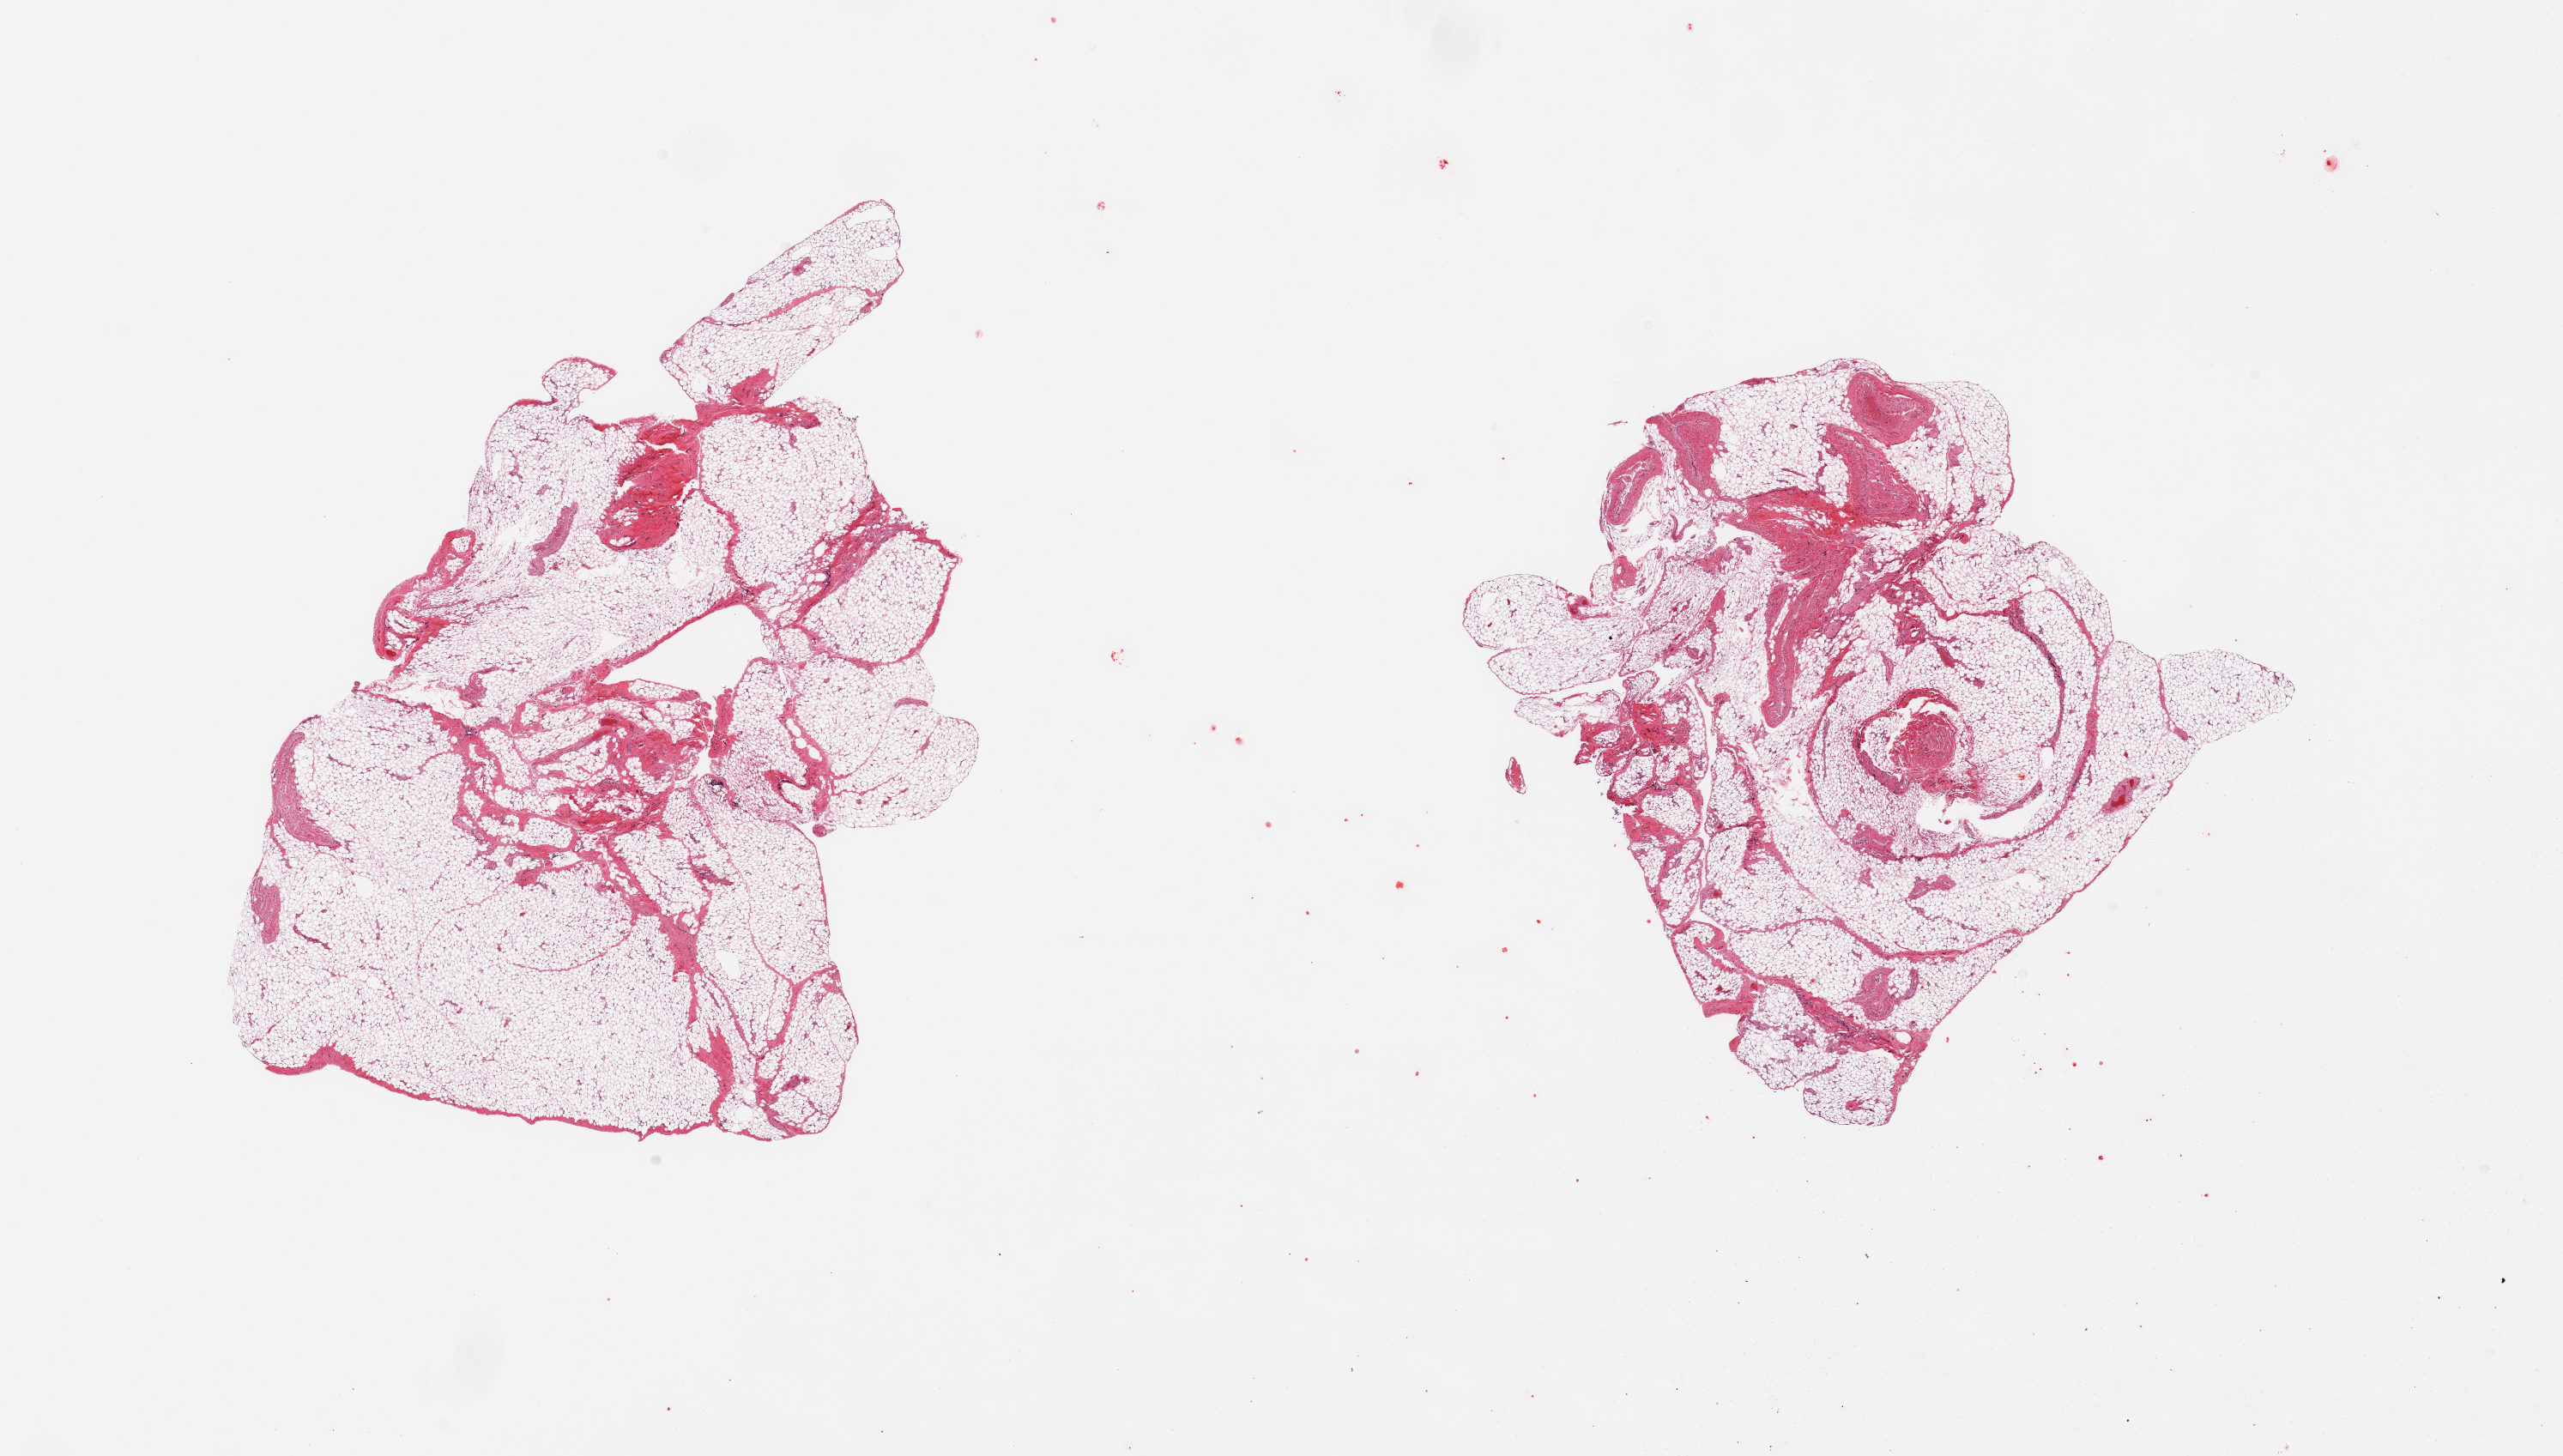
Haematoxylin and eosin whole-slide image — shown as a low-resolution overview of the whole scanned area (about 23.6 x 13.4 mm). PAXgene-fixed paraffin-embedded (PFPE) section. Section of omentum (target tissue). Donor tissue sample.
Pathologist's review note for this sample: 2 pieces; 5% & 10% fibrofatty, vascular, & neural content.